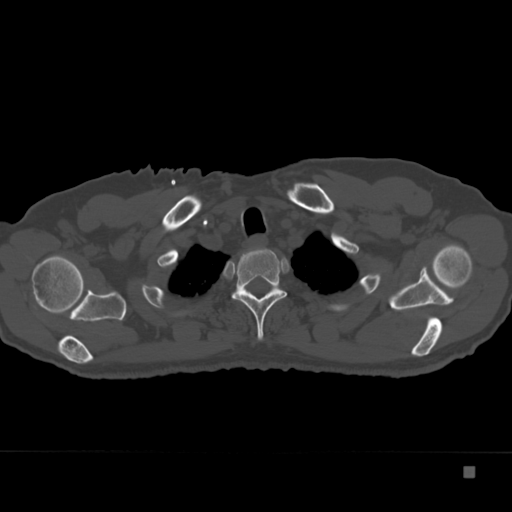
CT including the spine, one axial slice. Position 301 of 332 along the scan axis. 120 kVp. Bone window (W 1800 / L 400 HU). 1.5 mm slice thickness. 512 × 512 image matrix, field of view 389 × 389 mm. Male patient, age 72 years. Case-level facts recorded for this patient, not image findings: primary cancer: skeletal.
Structures marked on this image (semi-automatic segmentation, software-assisted and operator-edited):
- T2 vertebra: bounding box (x1, y1, x2, y2) in pixels: (232, 248, 287, 341)
- T3 vertebra: (242, 282, 279, 295)